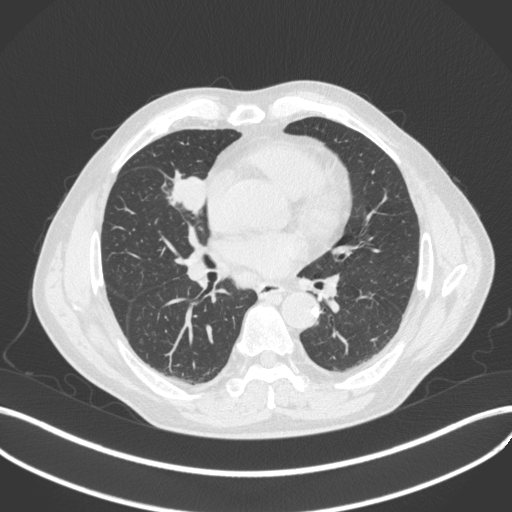
Chest CT, one axial slice; position 197 of 429 along the scan axis; 120 kVp; lung window (W 1500 / L -600 HU); 1 mm slice thickness; 512 × 512 image matrix, field of view 400 × 400 mm. Patient: male, 61 years. Case-level facts recorded for this patient, not image findings: clinical TNM (as recorded): T2b N1 M0.
Structures marked on this image (bounding box drawn by a radiologist):
- lung tumour (recorded histology: squamous cell carcinoma): bounding box <169,170,212,221> (left, top, right, bottom; pixels)